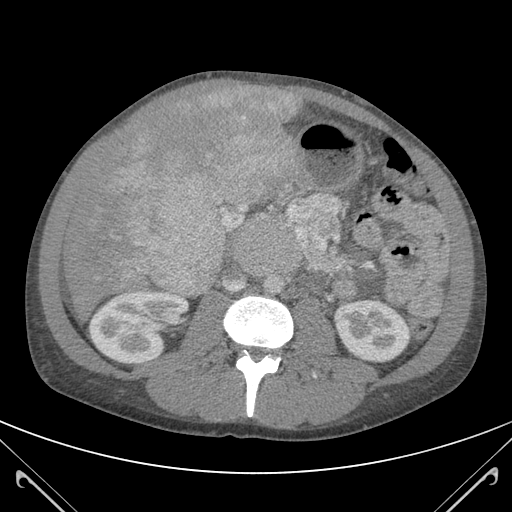
Contrast-enhanced abdominal CT (liver protocol), one axial slice; position 47 of 118 along the scan axis; soft-tissue window (W 400 / L 40 HU); 512 × 512 image matrix. Case-level facts recorded for this patient, not image findings: diagnosis: hepatocellular carcinoma (patient treated with transarterial chemoembolisation; whether this scan precedes or follows treatment is not stated here); TNM stage (as recorded): Stage-IIIB; Child-Pugh class: A; tumour nodularity: uninodular.
Outlined on this slice (semi-automatic segmentation, software-assisted and operator-edited):
- abdominal aorta: bounding box (x1, y1, x2, y2) in pixels: (265, 275, 284, 296)
- liver parenchyma outside the tumour (the mass and vessels are separate outlines, so this box may not span the whole liver): (62, 86, 287, 314)
- mass: (96, 86, 301, 292)